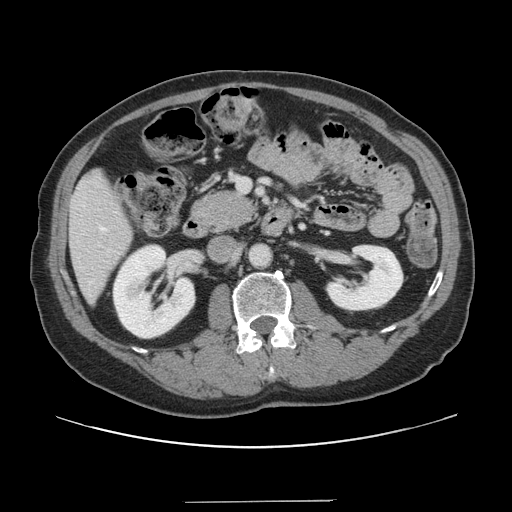
Contrast-enhanced abdominal CT, one axial slice; 120 kVp; intravenous contrast given; soft-tissue window (W 400 / L 40 HU); 512 × 512 image matrix. Male patient, age 63 years. Case-level facts recorded for this patient, not image findings: diagnosis: colorectal cancer liver metastases, imaged before liver resection; multiple liver metastases: no; largest metastasis: 2.1 cm; disease in both lobes: no.
Outlined on this slice (expert manual segmentation):
- hepatic veins: bounding box [x1, y1, x2, y2] px = [100, 227, 106, 231]
- liver: [70, 172, 132, 300]
- planned liver remnant (the part of the liver to remain after resection): [70, 172, 132, 300]
- portal vein (with intrahepatic branches): [237, 178, 249, 192]